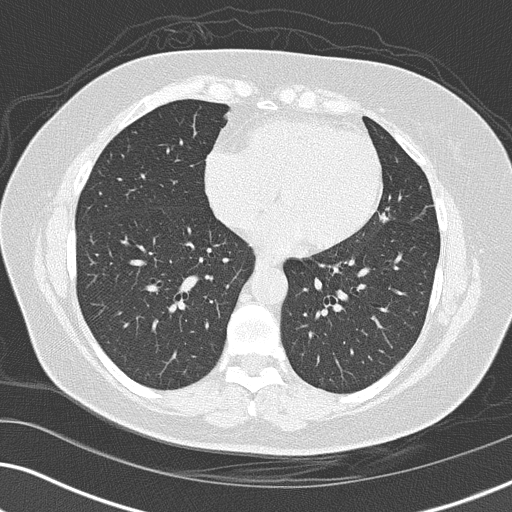
Chest CT (low-dose screening protocol), one axial image, third annual screen, lung window (W 1500 / L -600 HU), 2 mm slice thickness, 120 kVp, slice 89 of 152 in the series. Female, age 56 years at enrolment. Former smoker at enrolment.
• Expert-annotated lung lesion, bounding box (x1, y1, x2, y2) in pixels: (358, 196, 410, 243).
• Reader record for this screening exam (exam-level; its link to the box is not recorded): non-calcified nodule or mass ≥4 mm, lingula, 14 × 14 mm, spiculated (stellate) margins, soft tissue attenuation, pre-existing on the prior screen: yes; interval growth: yes.
• Official screen result: positive, other.
• Participant outcome: lung cancer diagnosed 86 days after this screen — adenocarcinoma, NOS, left upper lobe, poorly differentiated (G3), stage IIIA (AJCC 6th edition), 15 mm at pathology.